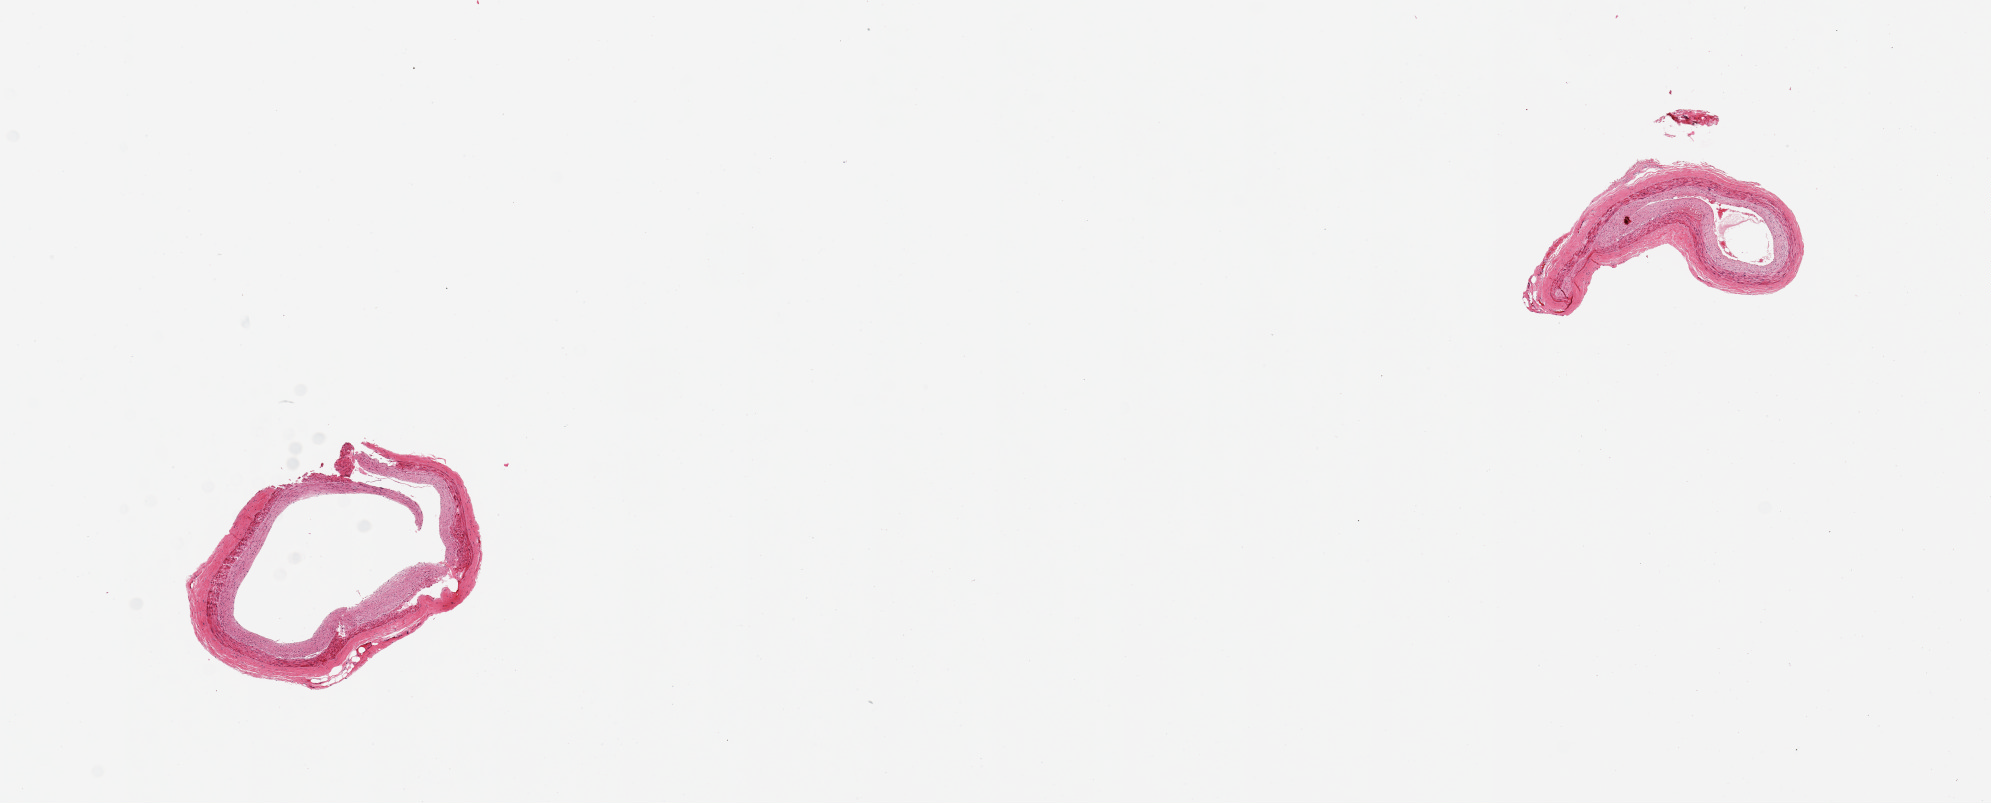
Hematoxylin and eosin (H&E) whole-slide image, a low-resolution overview of the entire scanned area, about 15.8 x 6.4 mm. PAXgene-fixed, paraffin-embedded tissue. Sampled site (target tissue): coronary artery. Tissue donor sample. Donor: male.
Review note (as recorded): 2 pieces.